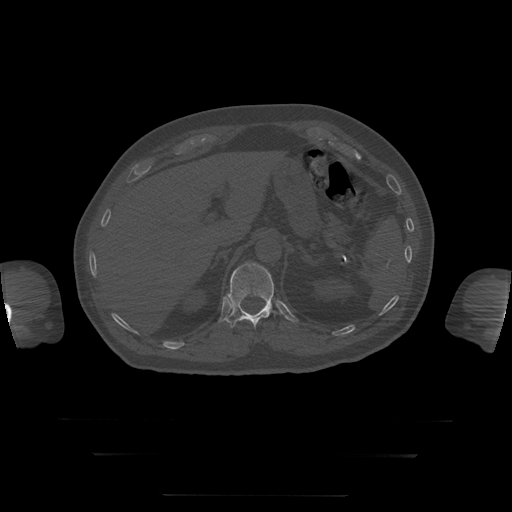
CT including the spine, one axial slice. Slice 76 of 397 in the series (ordered by position). Bone window (W 1800 / L 400 HU). 512 × 512 image matrix, field of view 510 × 510 mm. Patient age 73 years. Case-level facts recorded for this patient, not image findings: primary cancer: prostate.
Outlined on this slice (semi-automatic segmentation, software-assisted and operator-edited):
- T12 vertebra: bounding box <228,263,282,328> (left, top, right, bottom; pixels)